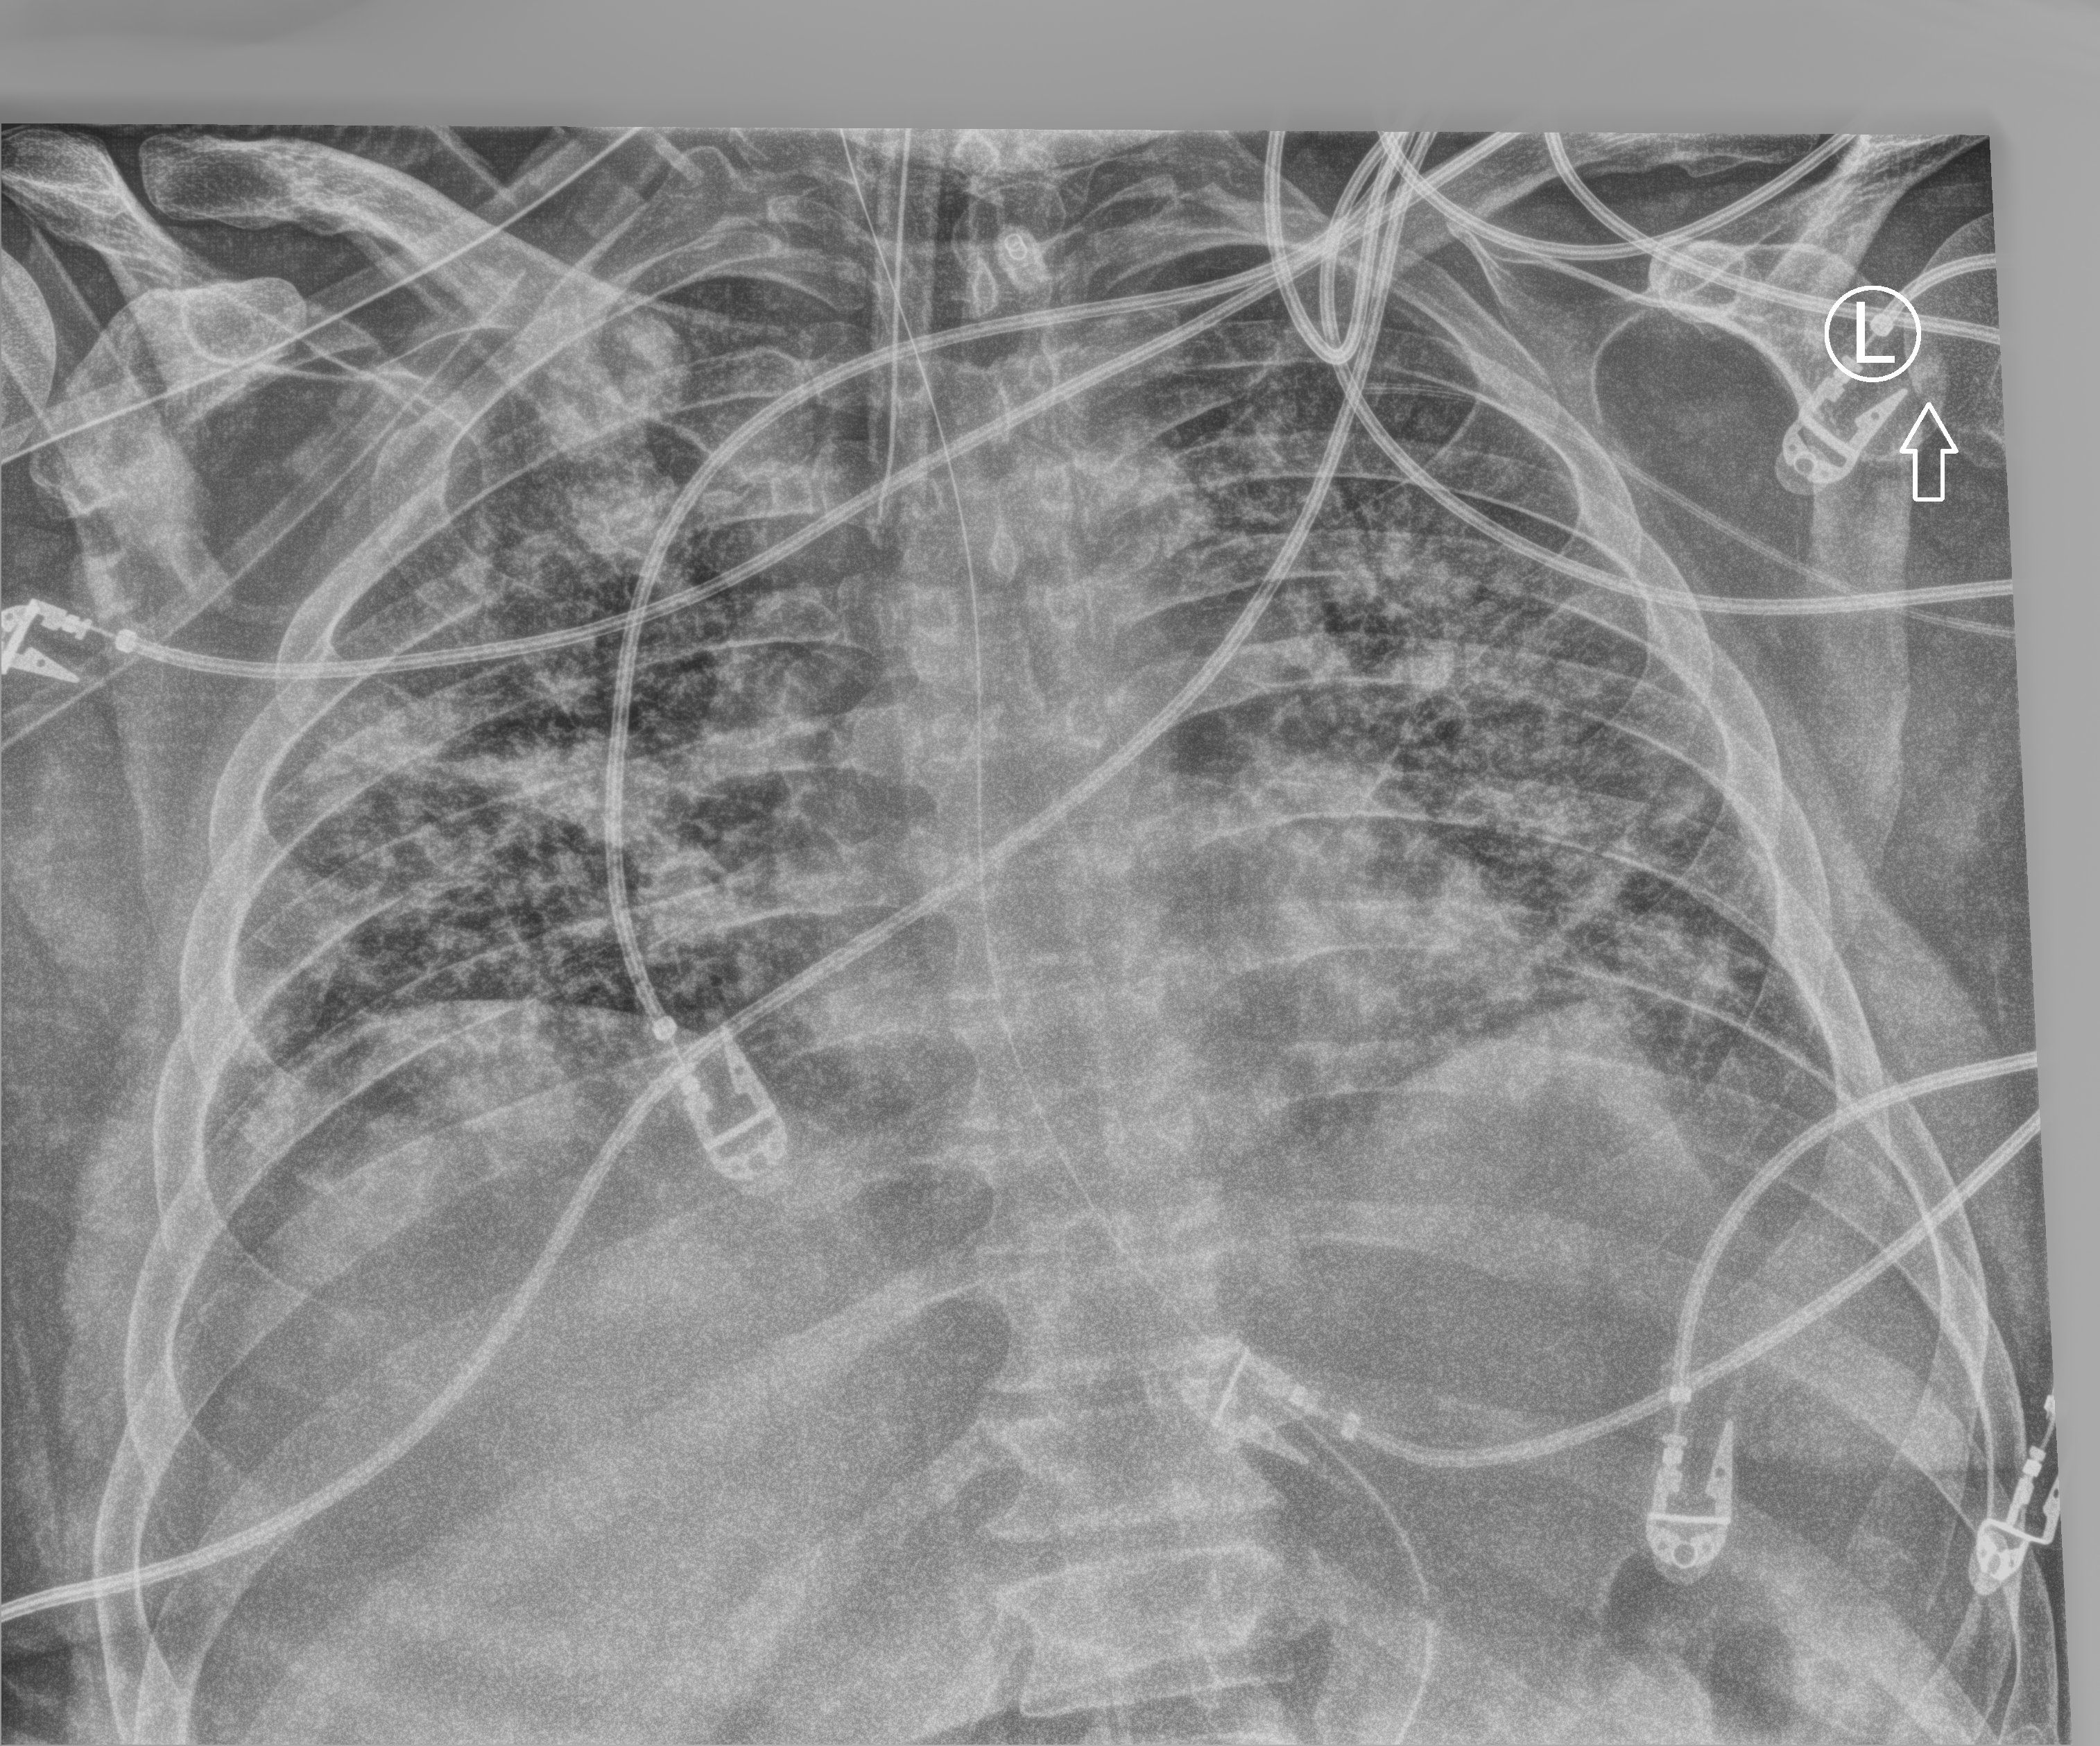
Portable chest radiograph. Adult patient hospitalised with COVID-19, age 18–59 years.
Hospital-stay facts (about this admission, not read from this image; timing relative to this image not recorded):
- length of hospital stay: 31 days
- admitted to intensive care during this hospital stay: yes